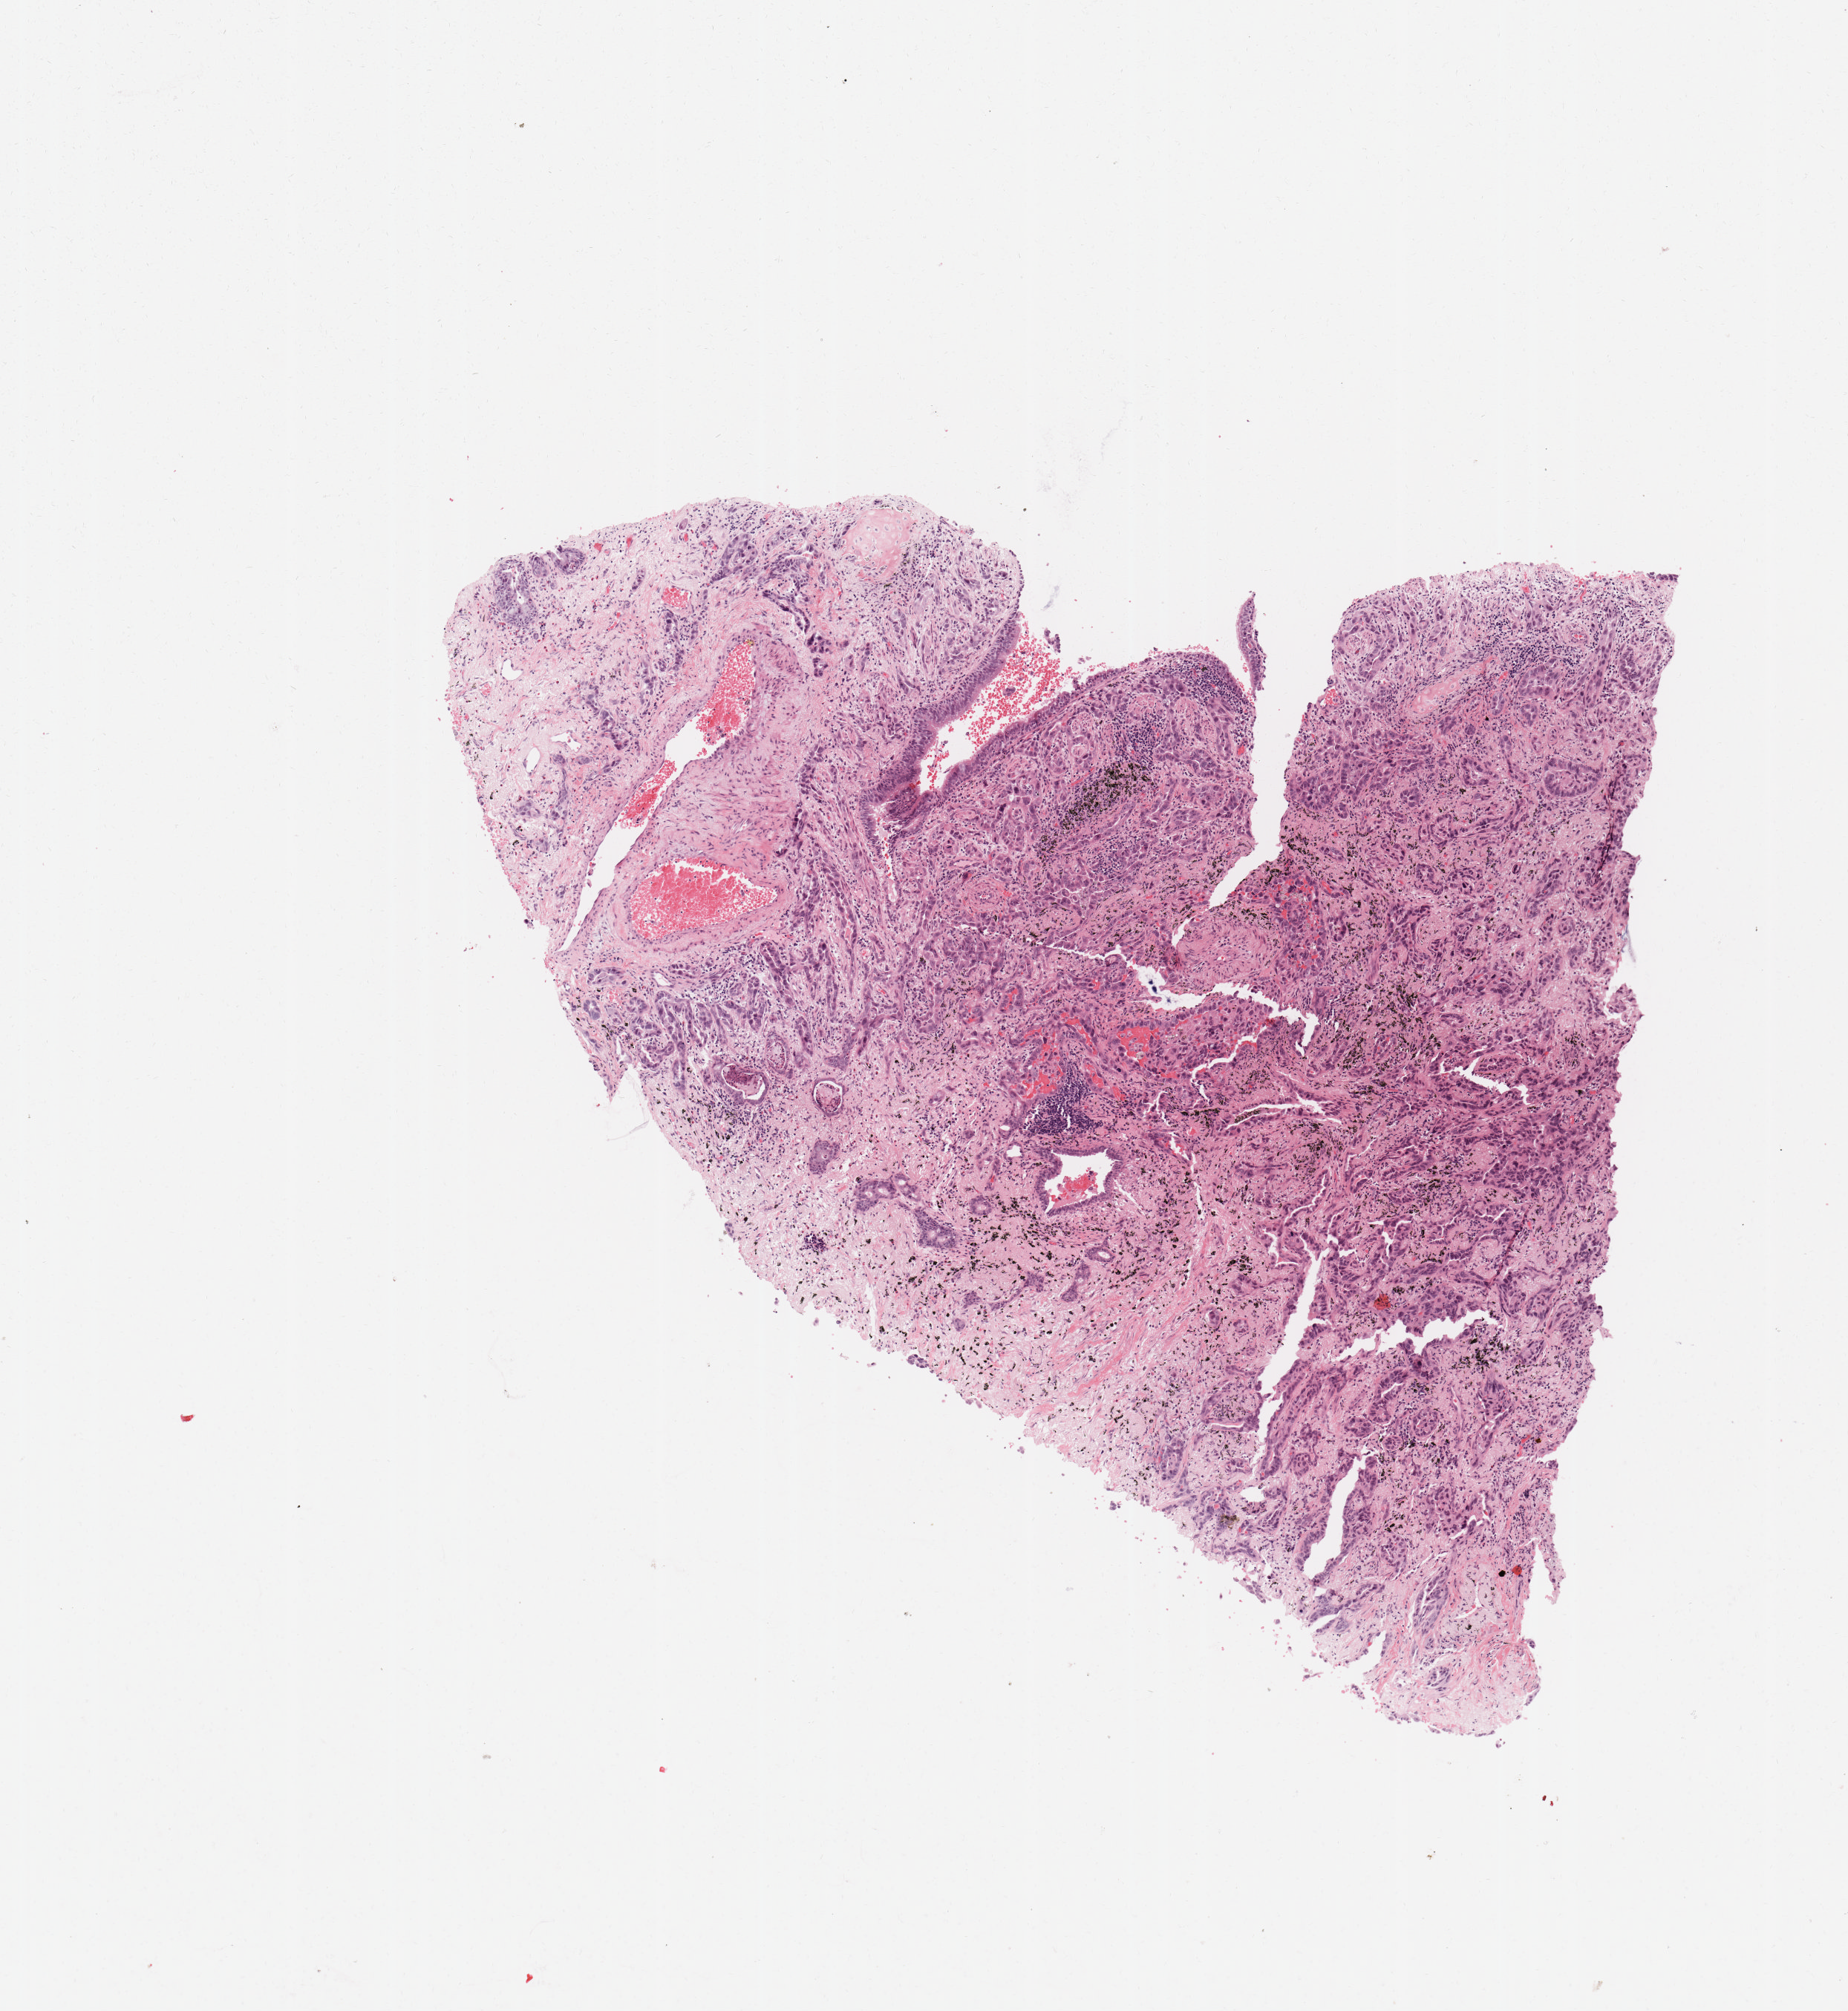
H&E whole-slide image, a low-resolution overview of the entire scanned area, about 4.9 x 5.4 mm (from a 20x scan); tumour tissue sample, lung. 61-year-old male patient. Histologic grade: G2 (moderately differentiated).
- AJCC pathologic stage: IIB
- diagnosis: Adenocarcinoma, NOS